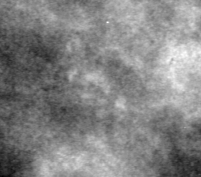
Region of interest cut from a scanned film mammogram (one marked finding), left breast, CC view.
- Finding: calcifications, morphology pleomorphic, distribution clustered; BI-RADS assessment category 4; pathology (as recorded): benign.